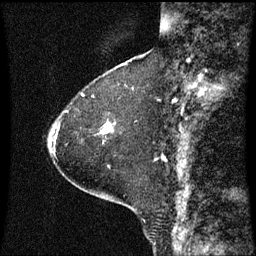
Breast MRI (dynamic contrast-enhanced), one sagittal slice; position 20 of 60 along the scan axis; dynamic contrast-enhanced series, image 2 of 3 at this slice position (ordered by acquisition); 1.5 T; TE 4.2 ms, TR 8.9 ms; 2 mm slice thickness; 256 × 256 image matrix. Female patient, age 63 years. Case-level facts recorded for this patient, not image findings: setting: breast cancer imaged before/during neoadjuvant chemotherapy; receptor status: HR-positive, HER2-negative.
Outlined on this slice (semi-automatically segmented with operator editing):
- analysis volume of interest (the breast-tissue region the enhancement analysis was run in; not a lesion): bounding box <101,122,111,135> (left, top, right, bottom; pixels)
- tumour enhancement mask (voxels above the 70 % enhancement threshold inside the analysis volume of interest): <101,122,111,135>